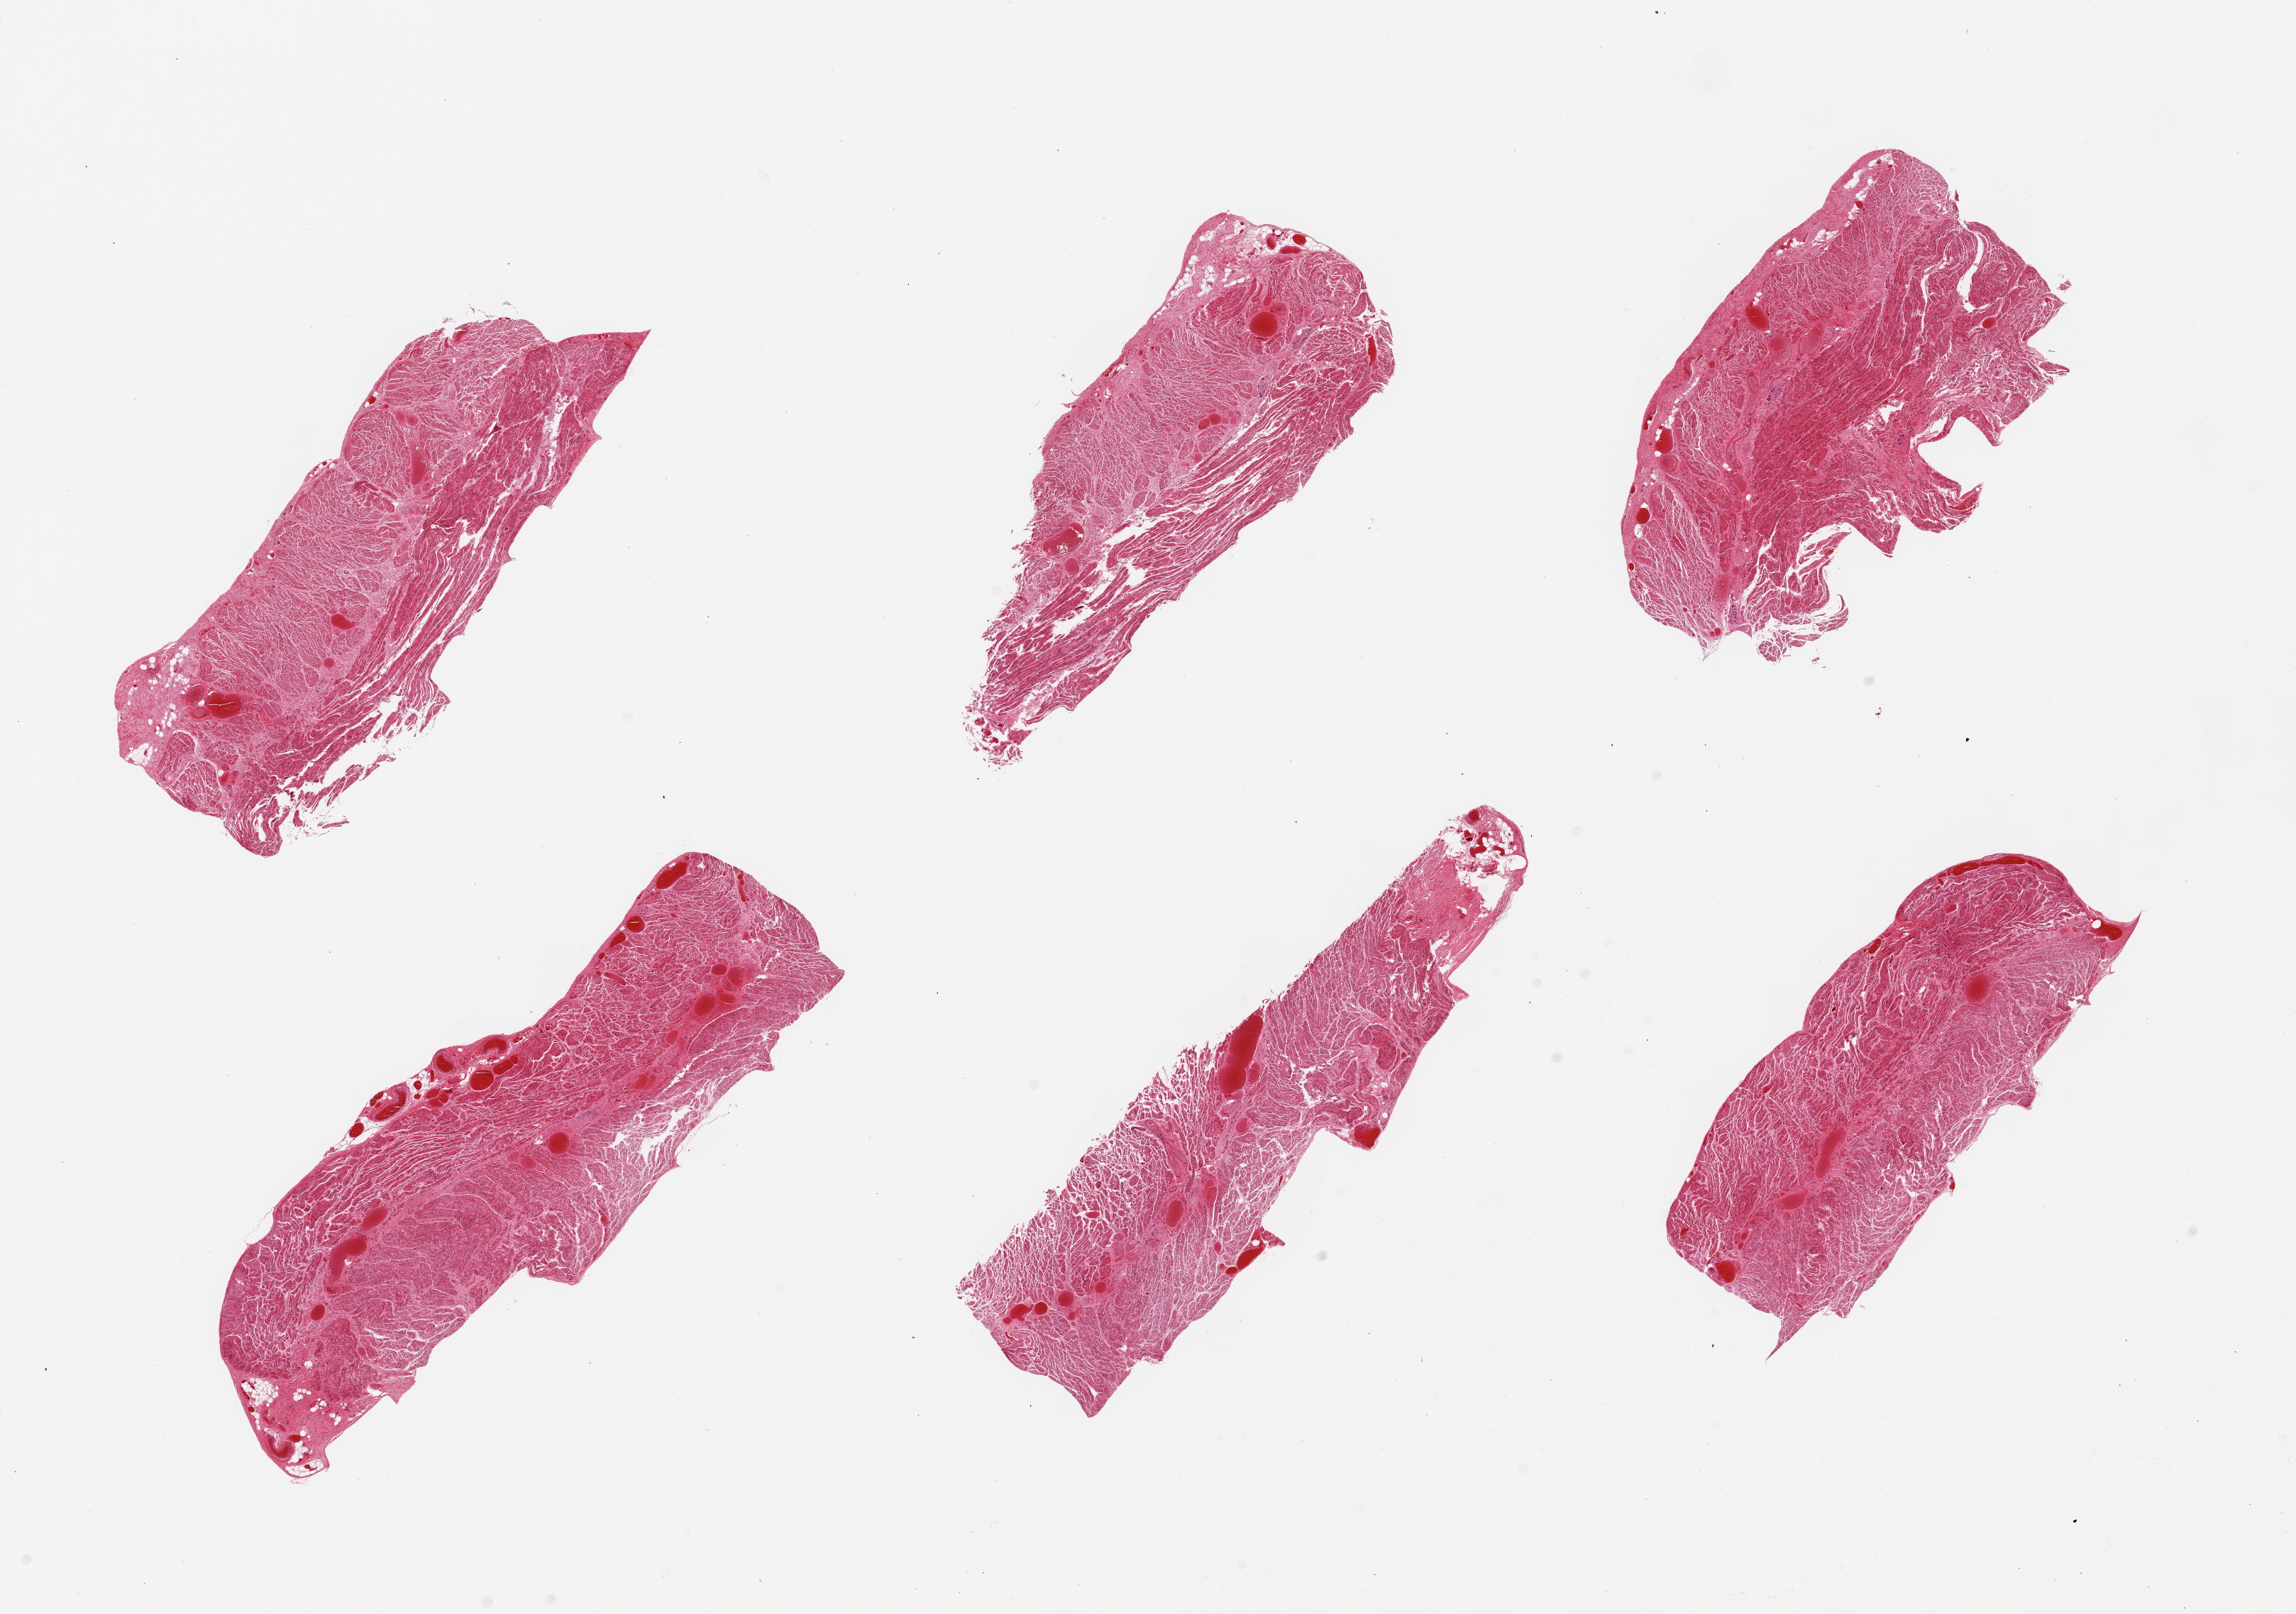
Whole-slide image, hematoxylin and eosin (H&E) stain, low-resolution overview of the scanned area, about 25.6 x 18.0 mm (acquisition: 20x scan). PAXgene-fixed paraffin-embedded (PFPE) section. Sampled site (target tissue): gastroesophageal junction. Donor tissue sample. Donor: male.
Review note (as recorded): 6 pieces; moderate vascular congestion.